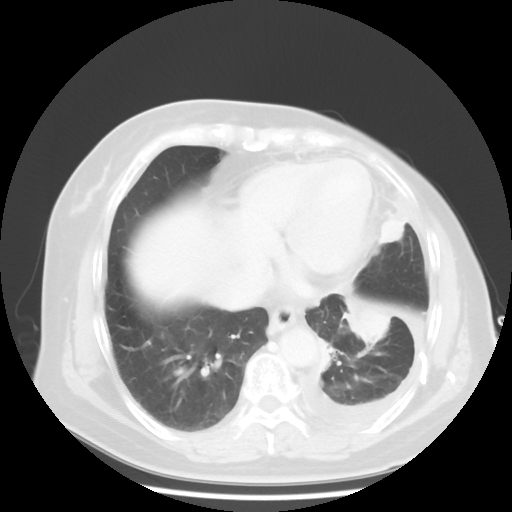
Chest CT, one axial slice. Slice 14 of 48 in the series (ordered by position). 120 kVp. Lung window (W 1500 / L -600 HU). 5 mm slice thickness. 512 × 512 image matrix, field of view 360 × 360 mm. Female patient, age 63 years. From the clinical record (not read from this slice): clinical TNM (as recorded): T2 N0 M1.
Annotated regions visible in this slice (rectangle marked by the reading radiologist):
- lung tumour (recorded histology: adenocarcinoma): bounding box <348,290,396,353> (left, top, right, bottom; pixels)